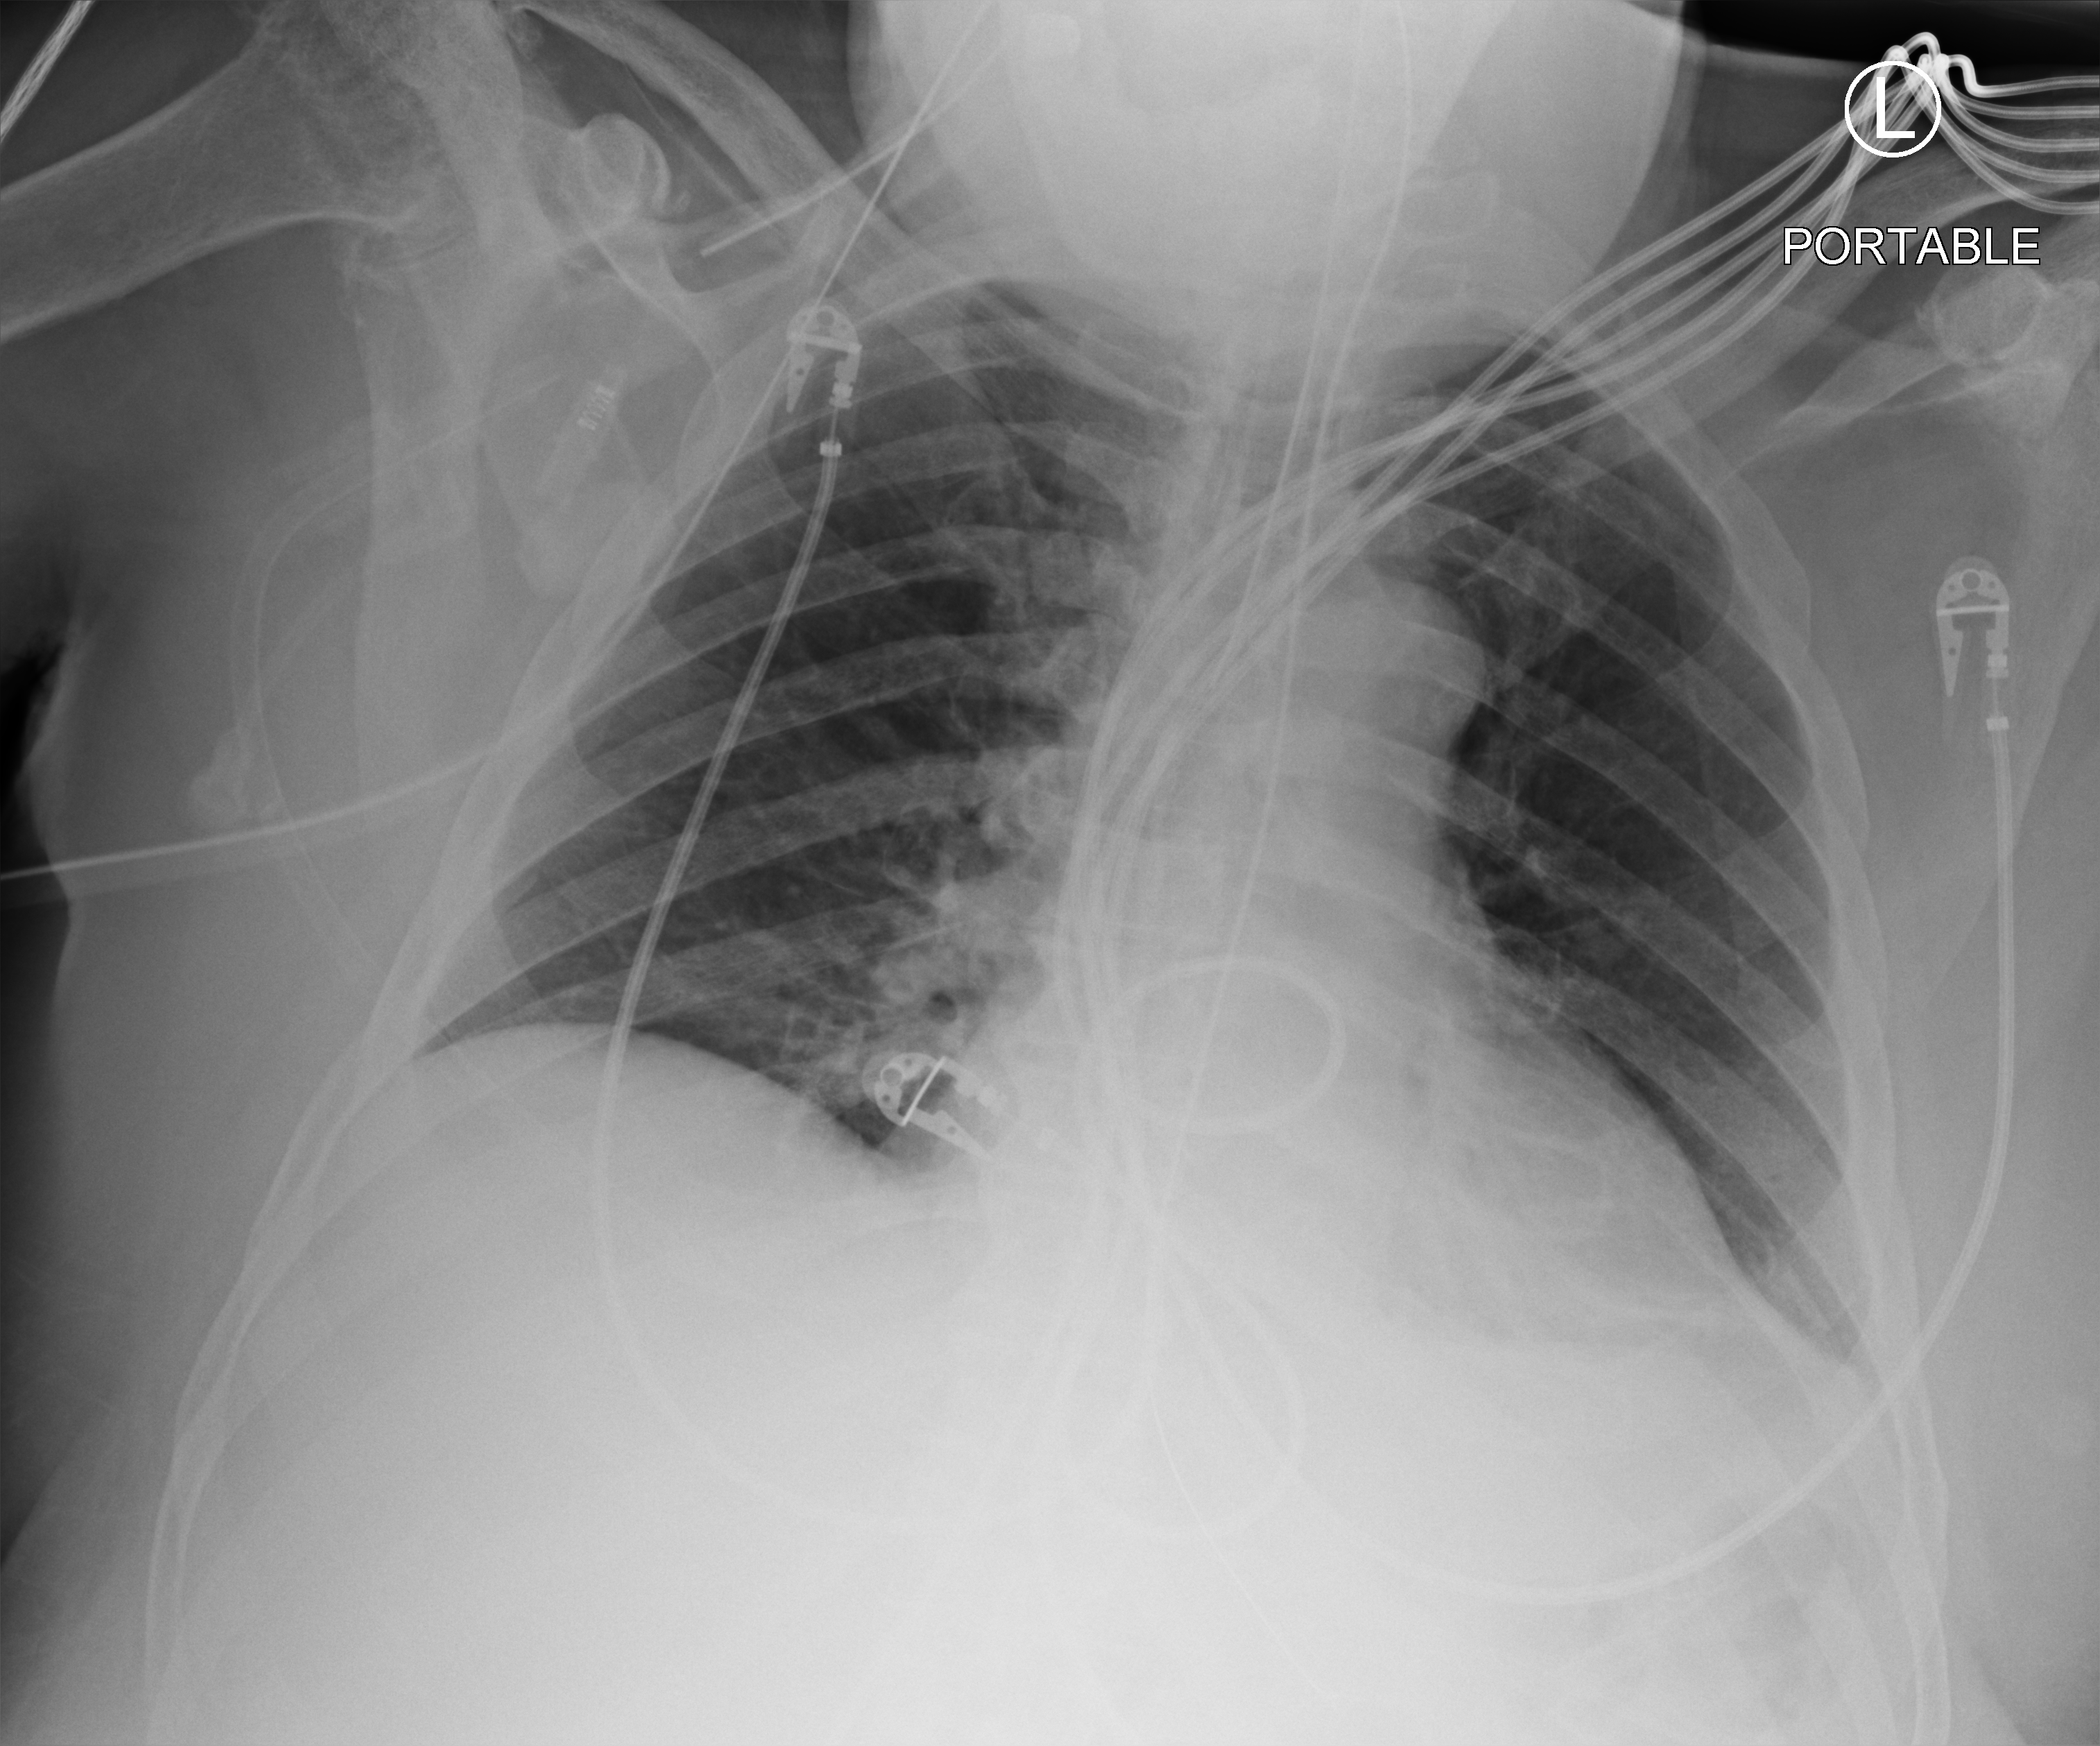
Bedside chest radiograph (computed radiography); anteroposterior (AP) projection. Patient hospitalised with COVID-19; male, aged 75–90 years.
Admission-level facts for this patient (not findings on this image; timing relative to this image not recorded):
- chronic kidney disease (admission record): no